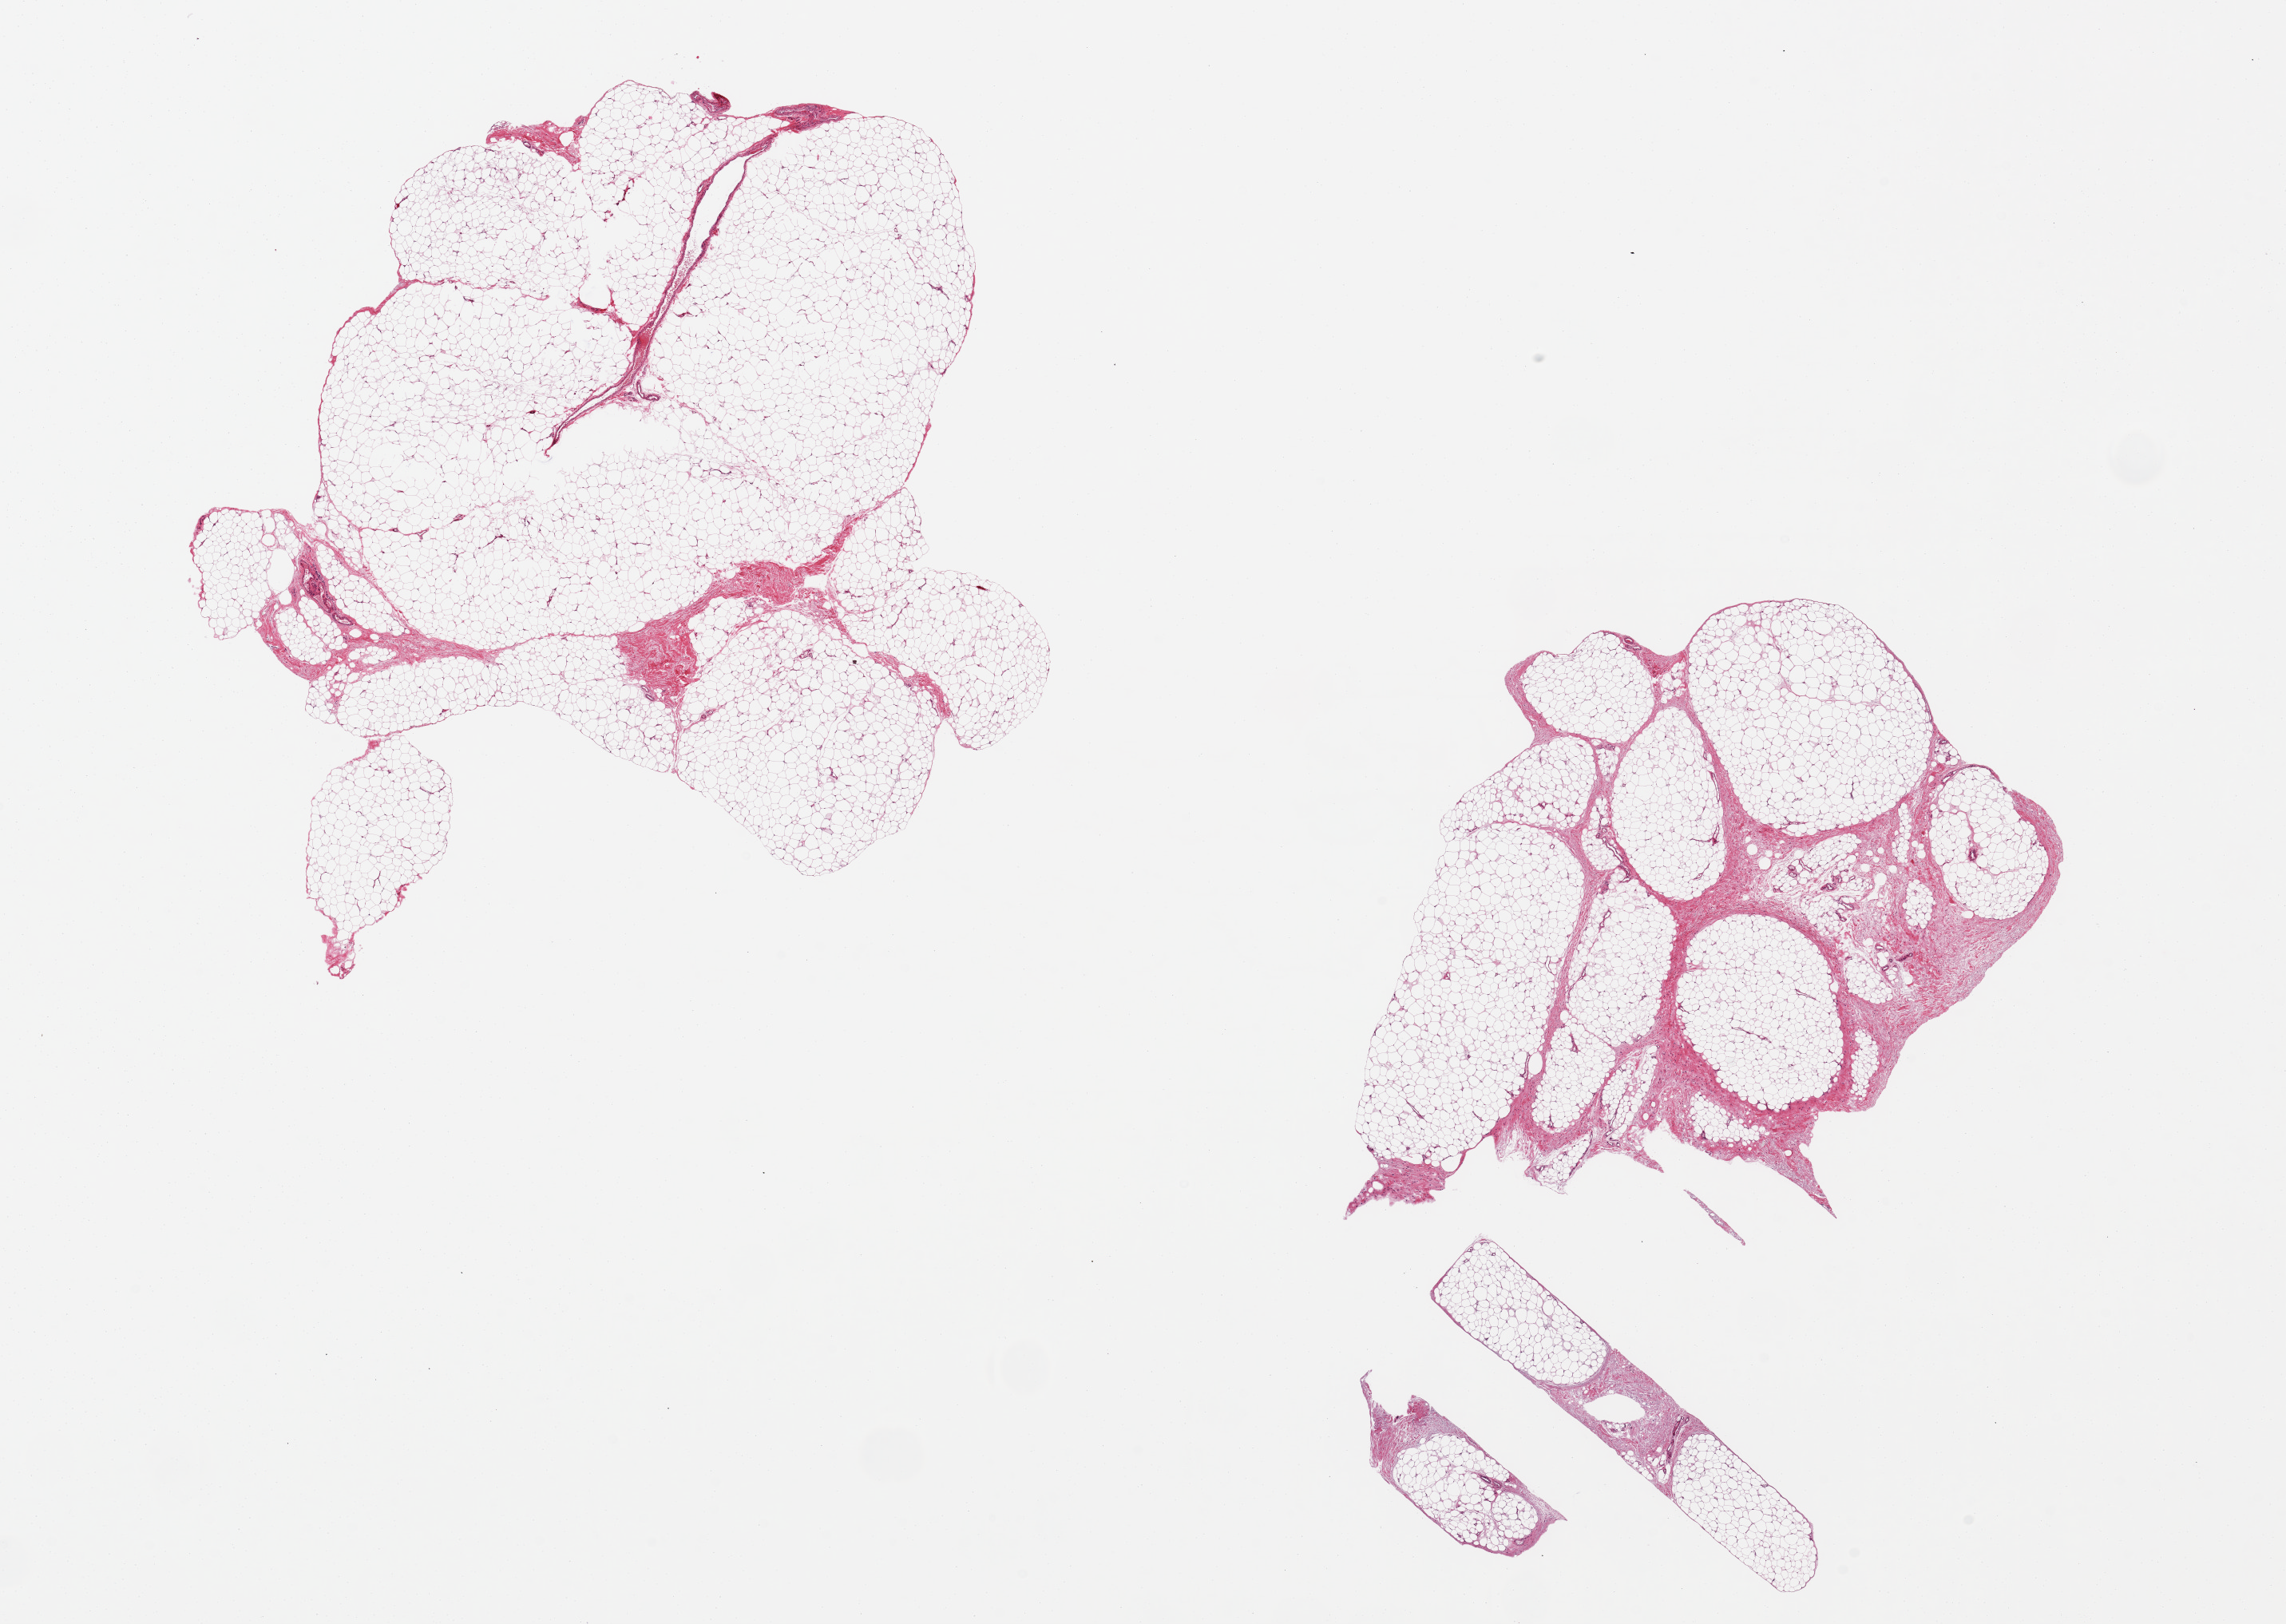
Whole-slide image, H&E stain, low-resolution overview of the scanned area, about 22.6 x 16.1 mm (slide scanned at 20x), PAXgene-fixed, paraffin-embedded tissue, section of adipose tissue (target tissue), donor tissue sample. Donor: male.
Pathologist's review note for this sample: 2 aliquots, ~8x6mm.